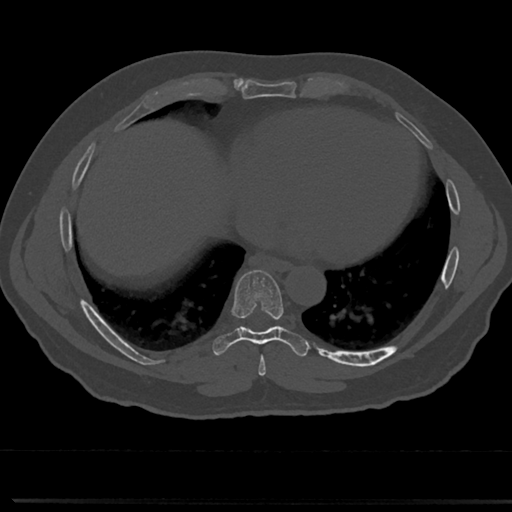
CT including the spine, one axial slice. Position 357 of 817 along the scan axis. Reconstruction kernel Br40s/3. 120 kVp. Bone window (W 1800 / L 400 HU). 0.5 mm slice thickness. 512 × 512 image matrix, field of view 355 × 355 mm. Male patient, age 61 years. From the clinical record (not read from this slice): primary cancer: prostate.
Annotated regions visible in this slice (semi-automatic segmentation, software-assisted and operator-edited):
- T7 vertebra: bounding box [x1, y1, x2, y2] px = [240, 329, 283, 363]
- T8 vertebra: [237, 270, 284, 336]